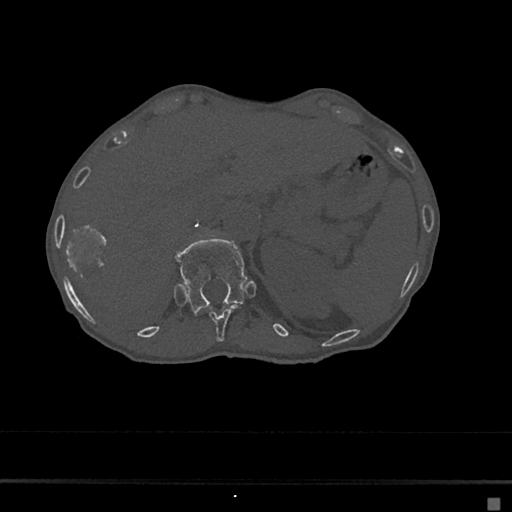
CT including the spine, one axial slice; position 137 of 797 along the scan axis; bone window (W 1800 / L 400 HU); 0.5 mm slice thickness; 512 × 512 image matrix. Female patient, age 68 years. From the clinical record (not read from this slice): primary cancer: renal.
Structures marked on this image (semi-automatically segmented with operator editing):
- T11 vertebra: bounding box <209,307,237,341> (left, top, right, bottom; pixels)
- T12 vertebra: <176,237,248,311>